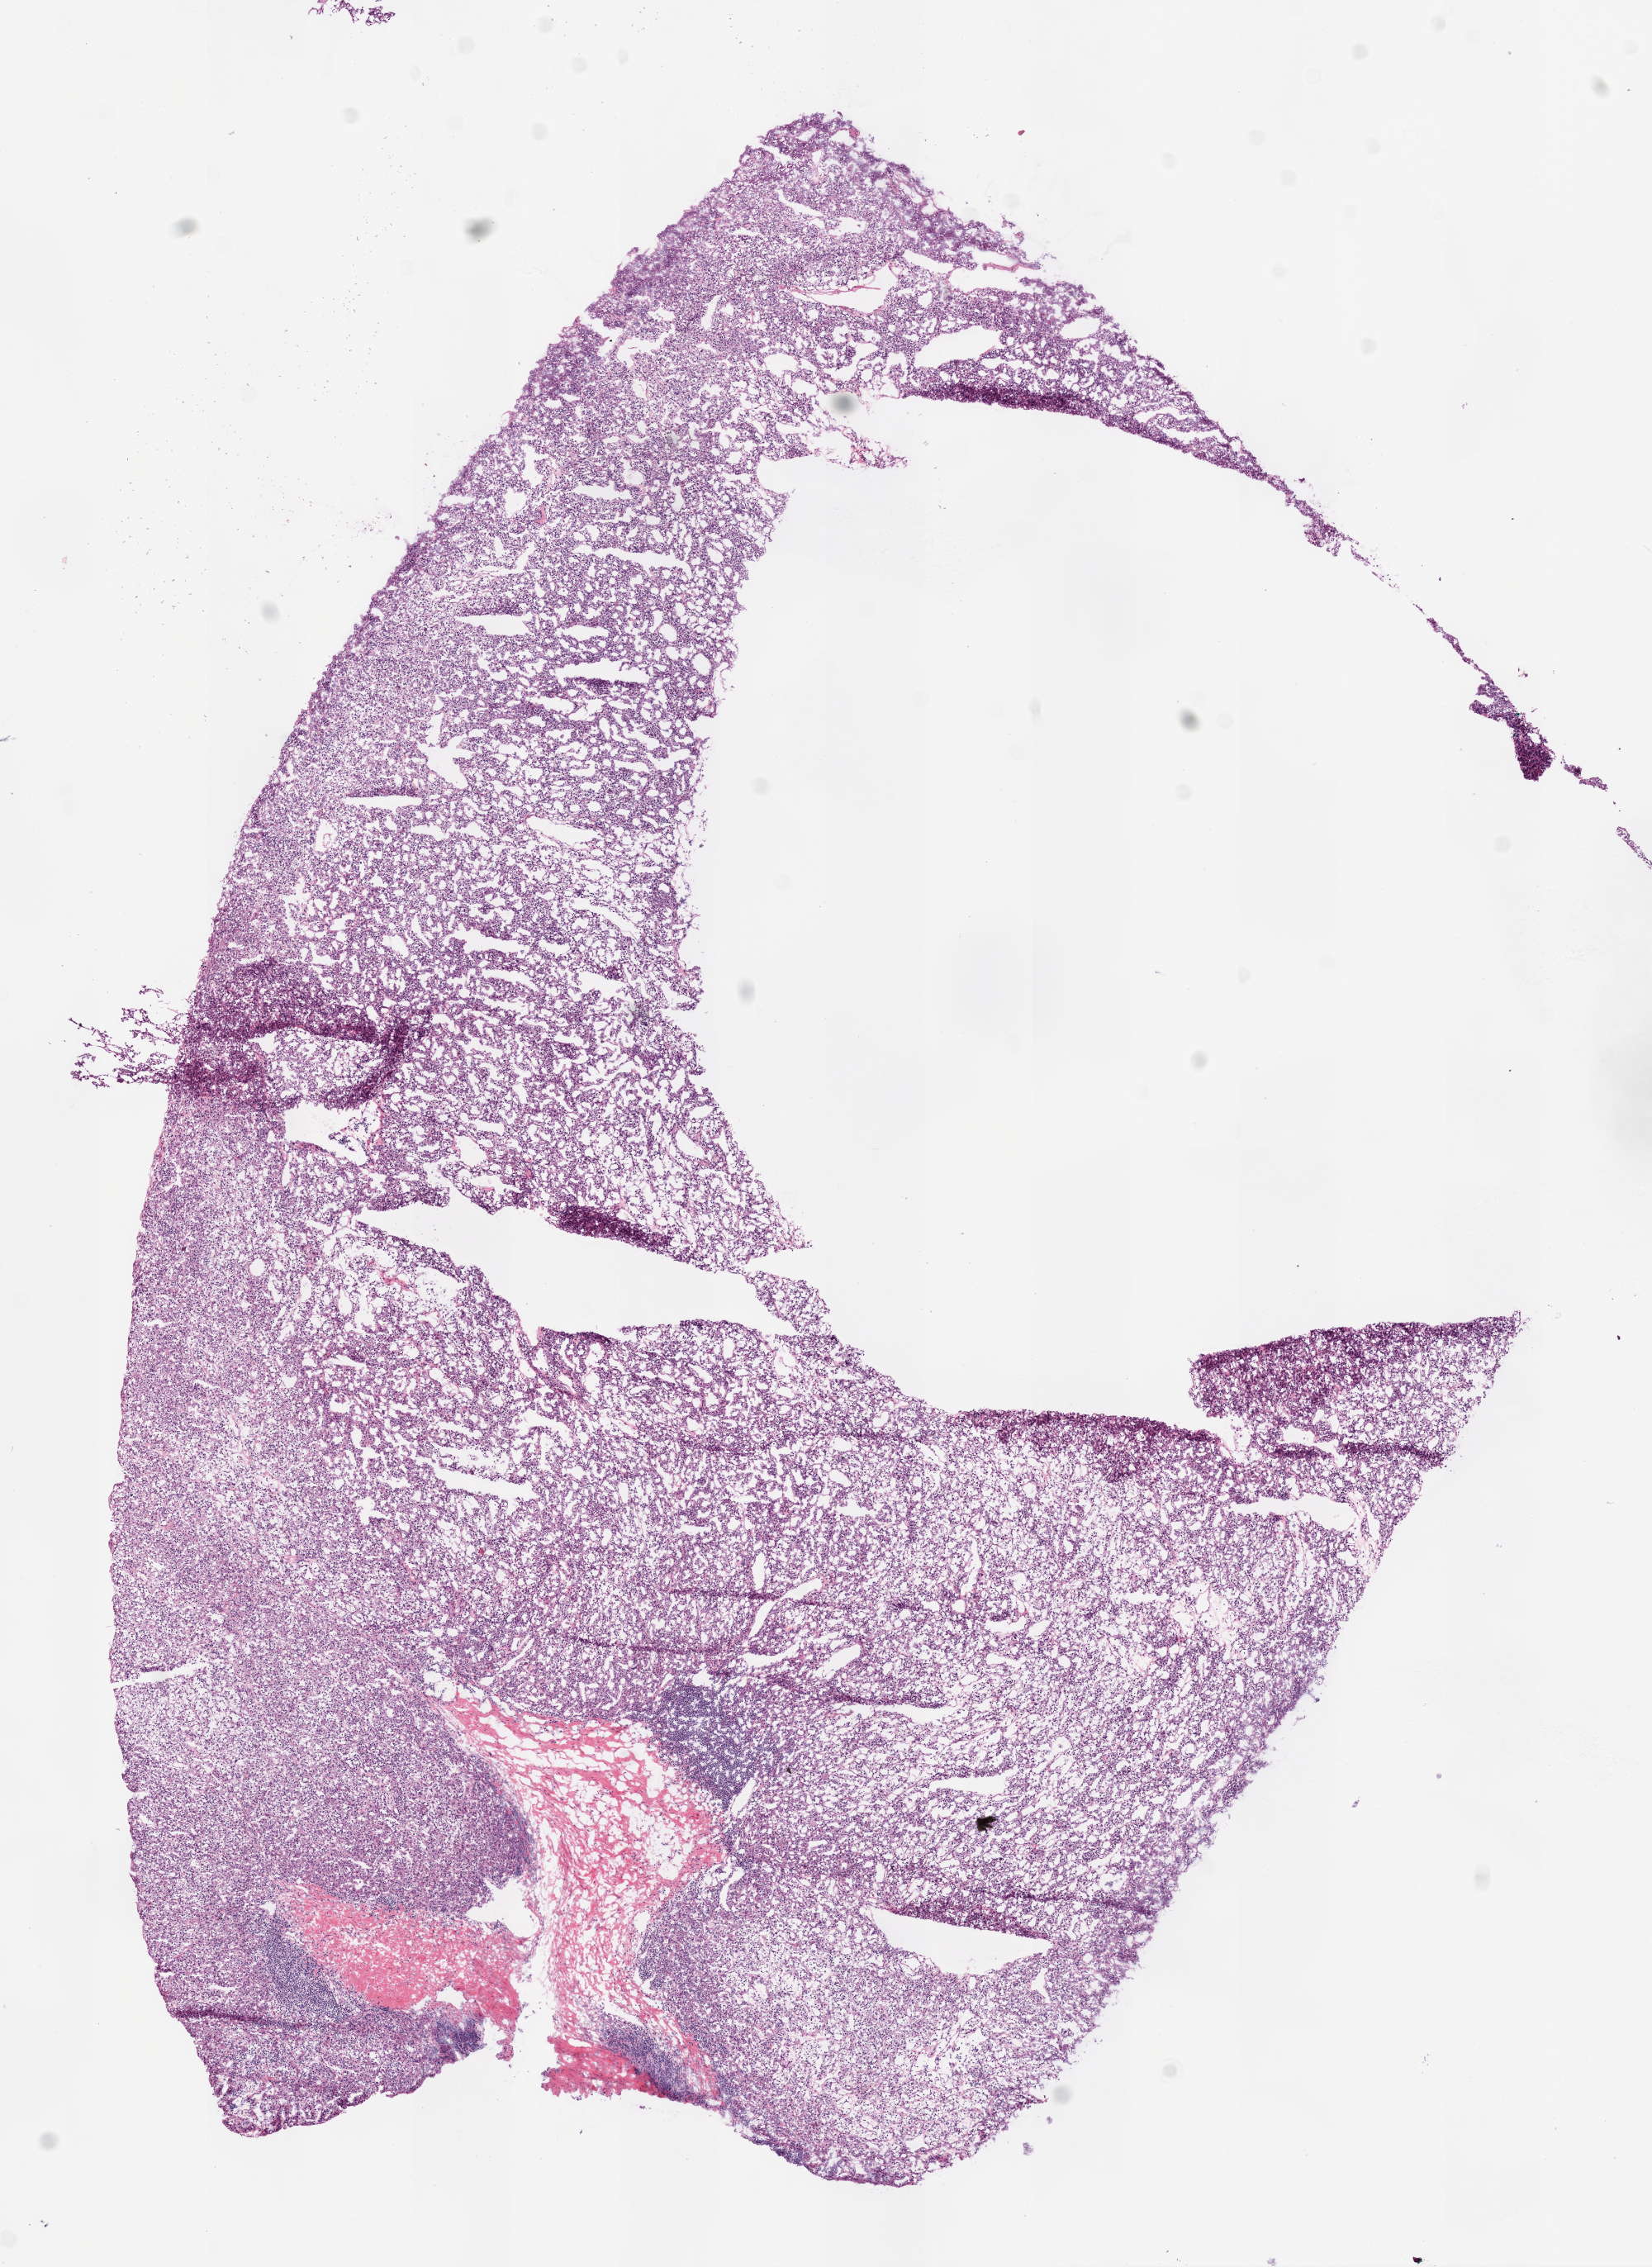
Whole-slide histology image, H&E, a low-resolution overview of the entire scanned area, about 8.0 x 11.0 mm (acquisition: 20x scan); frozen section from the bottom of the tissue portion; kidney, primary tumour sample. Female, age 54 years at initial diagnosis. Histologic grade: G2 (moderately differentiated). Composition of this section per pathologist review: tumour cells 82%, tumour nuclei 75%, normal cells 0%, stromal cells 8%, necrosis 0%.
Lymph nodes positive (case pathology): 0 of 5 examined. Pathologic diagnosis: Clear cell adenocarcinoma, NOS. TNM: T2 N0 M0. AJCC pathologic stage: II (7th edition).